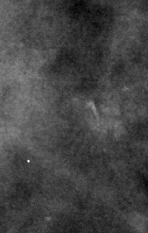
Cropped region of a digitized screen-film mammogram centred on a radiologist-marked abnormality; right breast; CC view; BI-RADS breast density category 4 (scale 1–4).
Marked abnormality: calcifications, morphology pleomorphic, distribution clustered; BI-RADS assessment category 4; pathology (as recorded): benign.